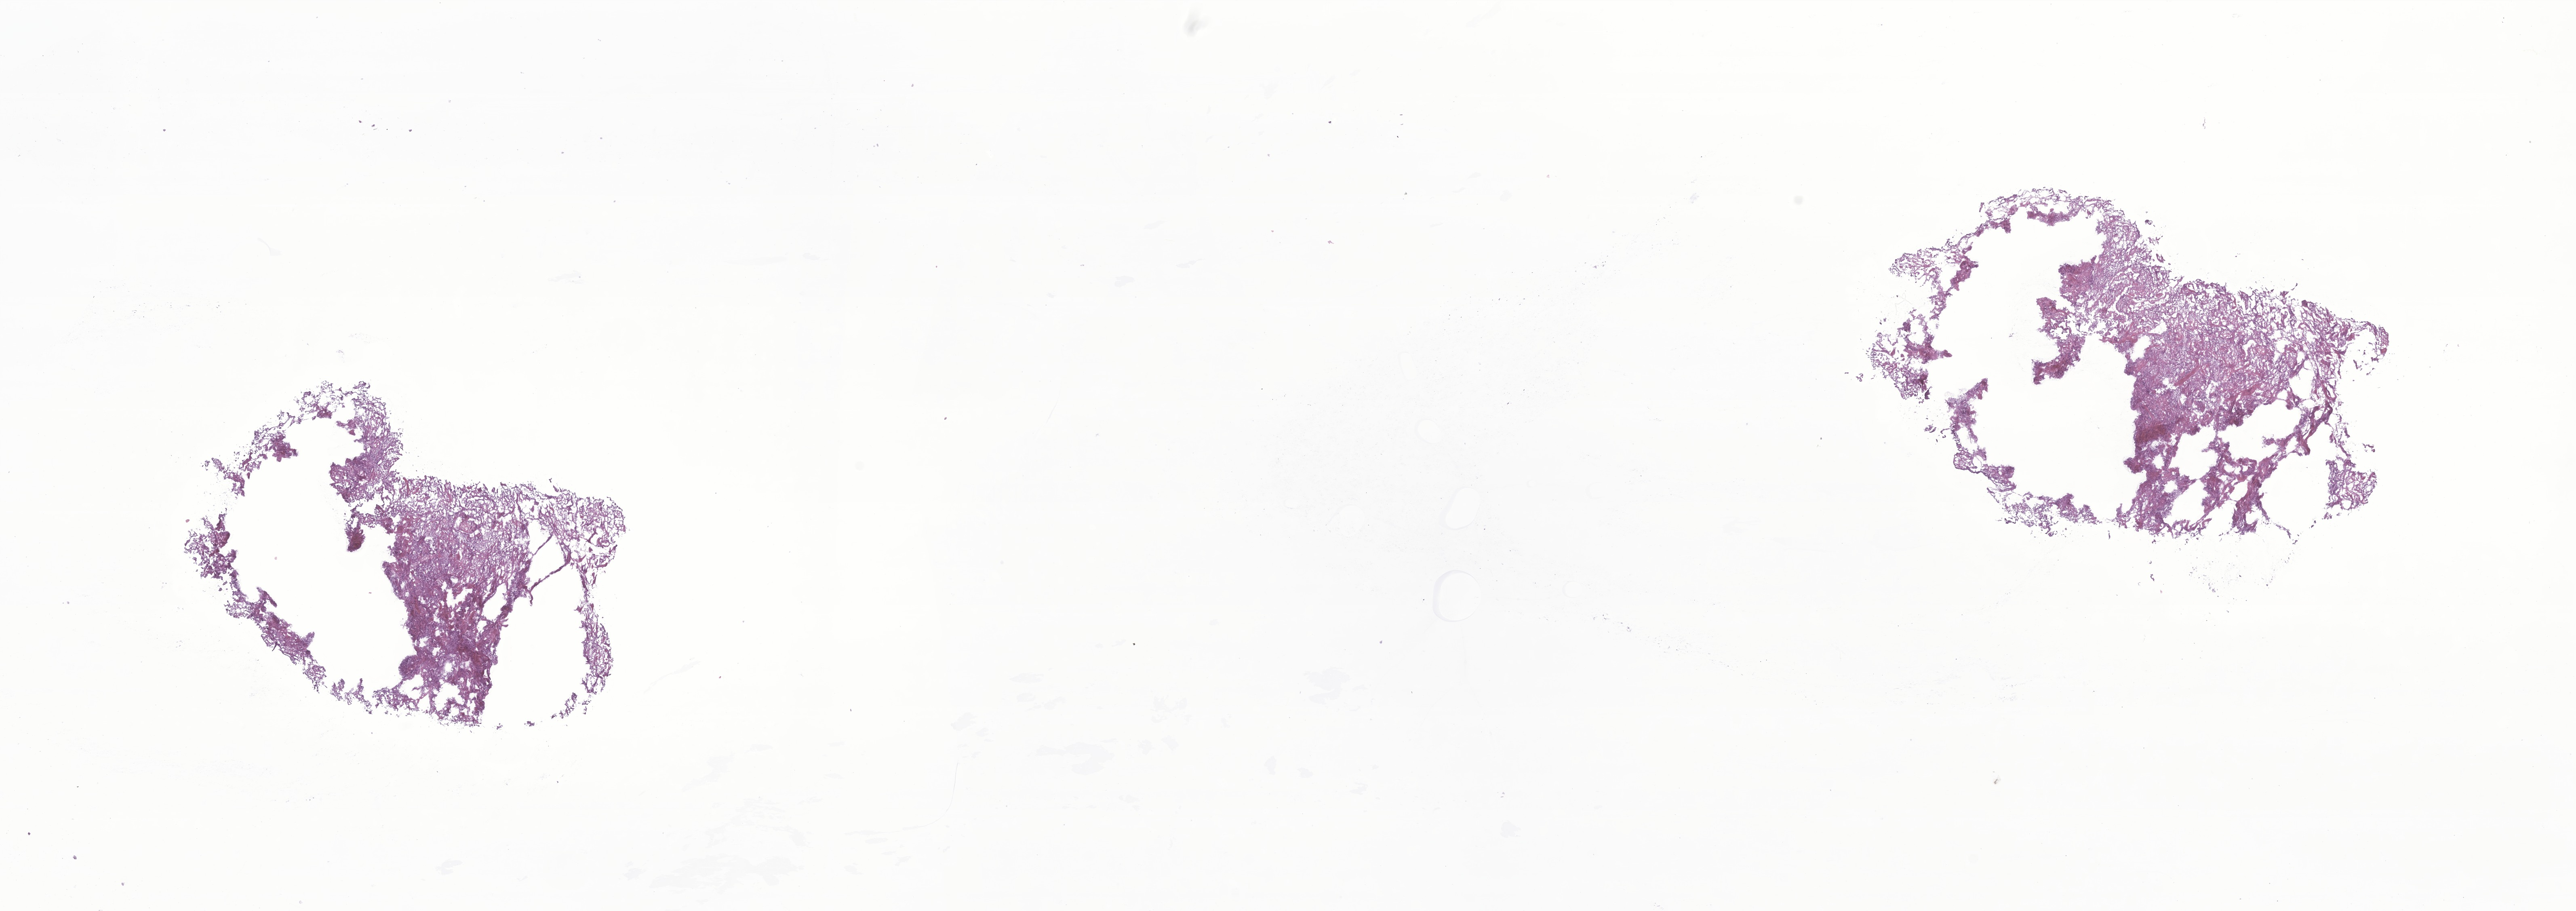
Haematoxylin and eosin whole-slide image of tumor tissue from the brain — low-resolution overview of the scanned area, about 26.9 x 9.5 mm, frozen section. Patient male; age 70 months (5 years 10 months).
Recorded diagnosis: Pilocytic astrocytoma.